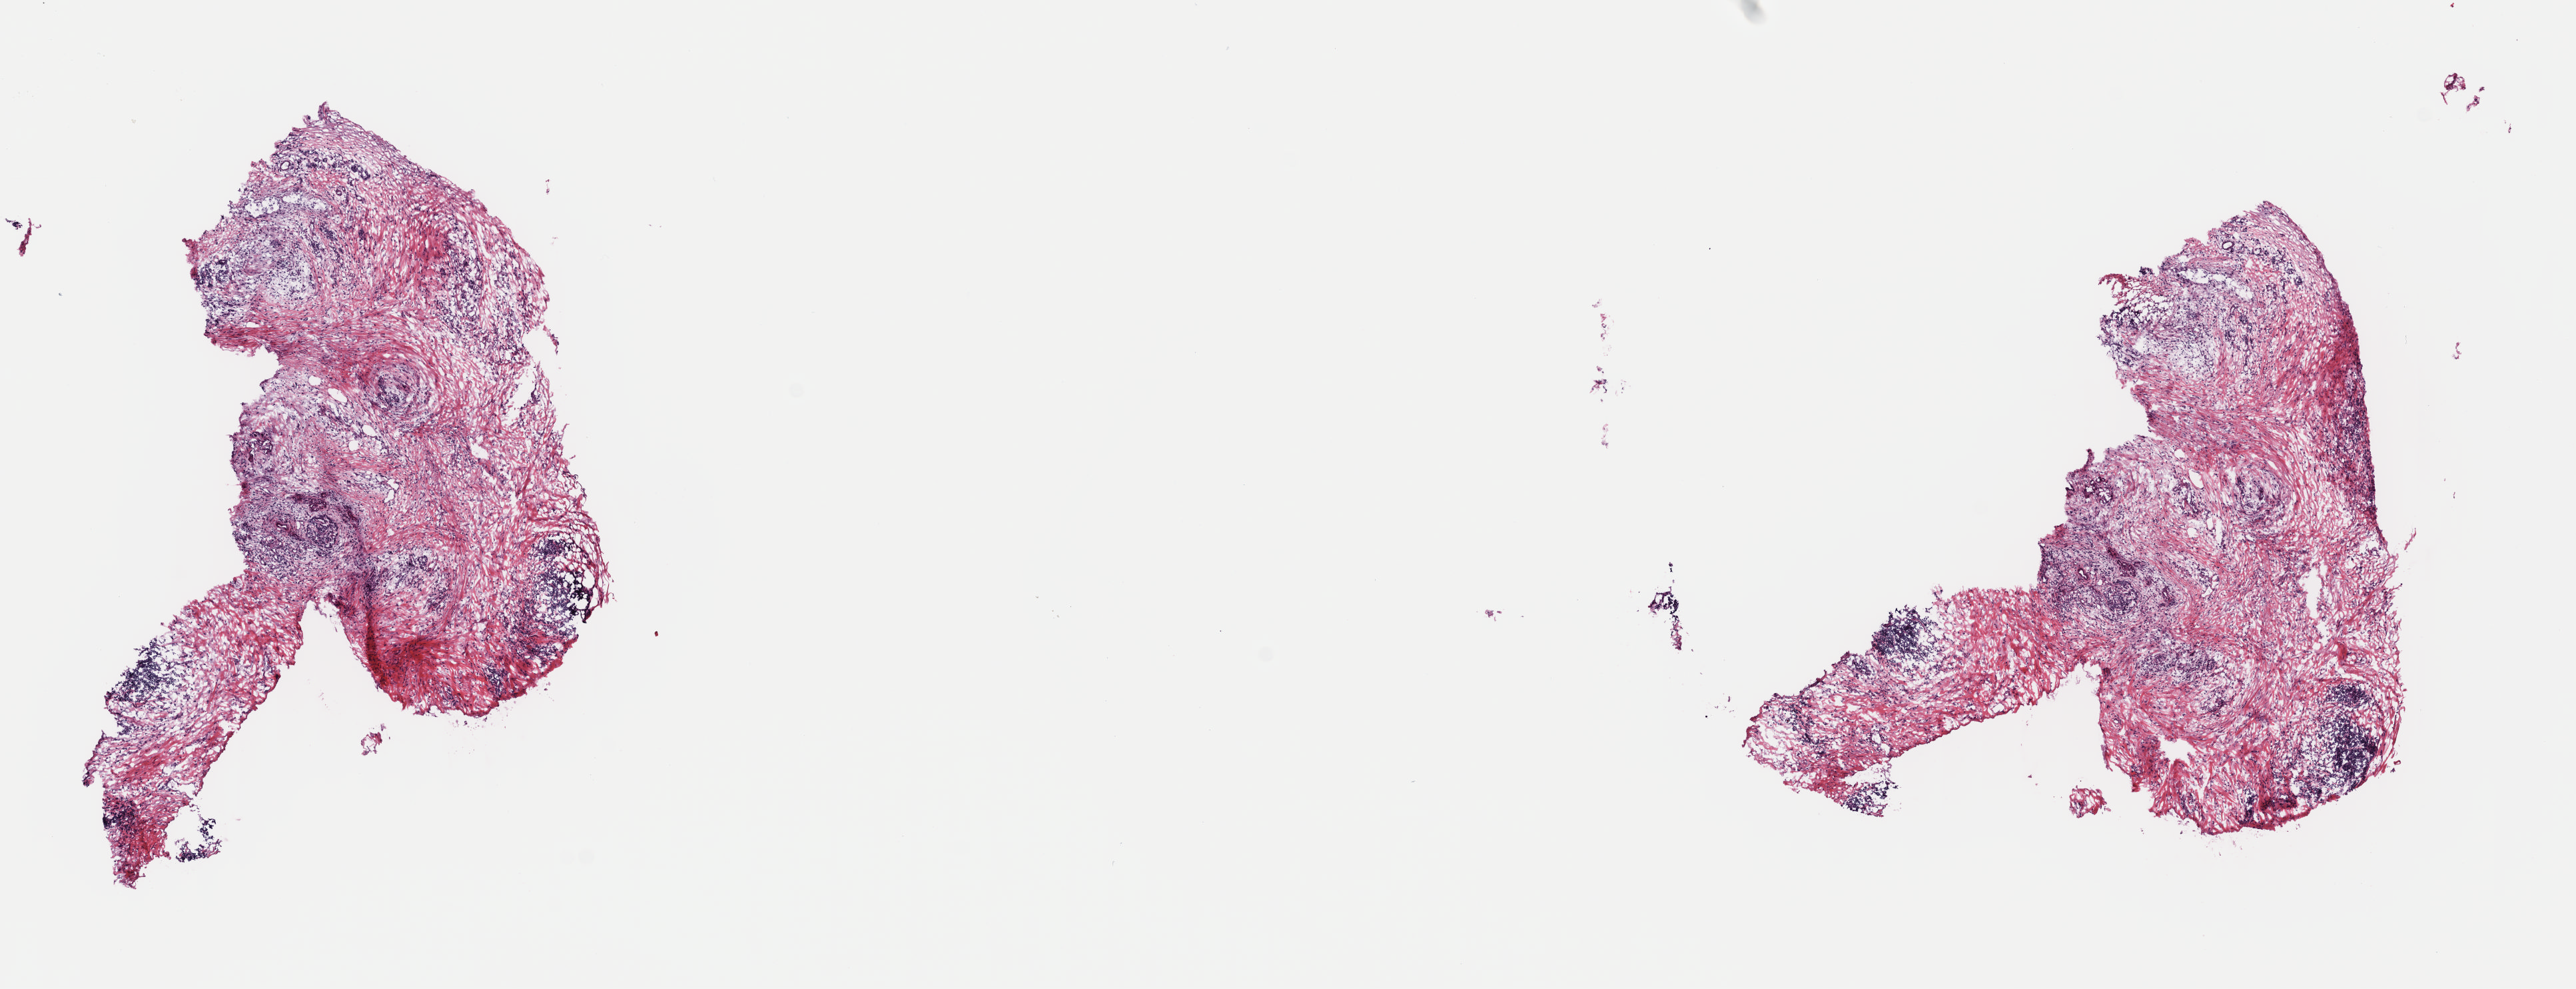
Whole-slide histology image, Hematoxylin and eosin (H&E) stained, whole scanned area (about 15.3 x 5.9 mm, acquisition: 40x scan) shown as a low-resolution overview, frozen section, sample: primary tumour, pancreas. Patient: female, age at initial diagnosis 81 years. Histologic grade: G2 (moderately differentiated). Pathologist review of this section (percent, as recorded): tumour cells 100%, tumour nuclei 15%, normal cells 0%, stromal cells 0%, necrosis 0%. Inflammatory infiltration, as recorded: lymphocyte infiltration 10%, monocyte infiltration 0%, neutrophil infiltration 0%.
Diagnosis: Infiltrating duct carcinoma, NOS (head of pancreas). TNM: T3 N1b MX. AJCC pathologic stage: IIB (7th edition).